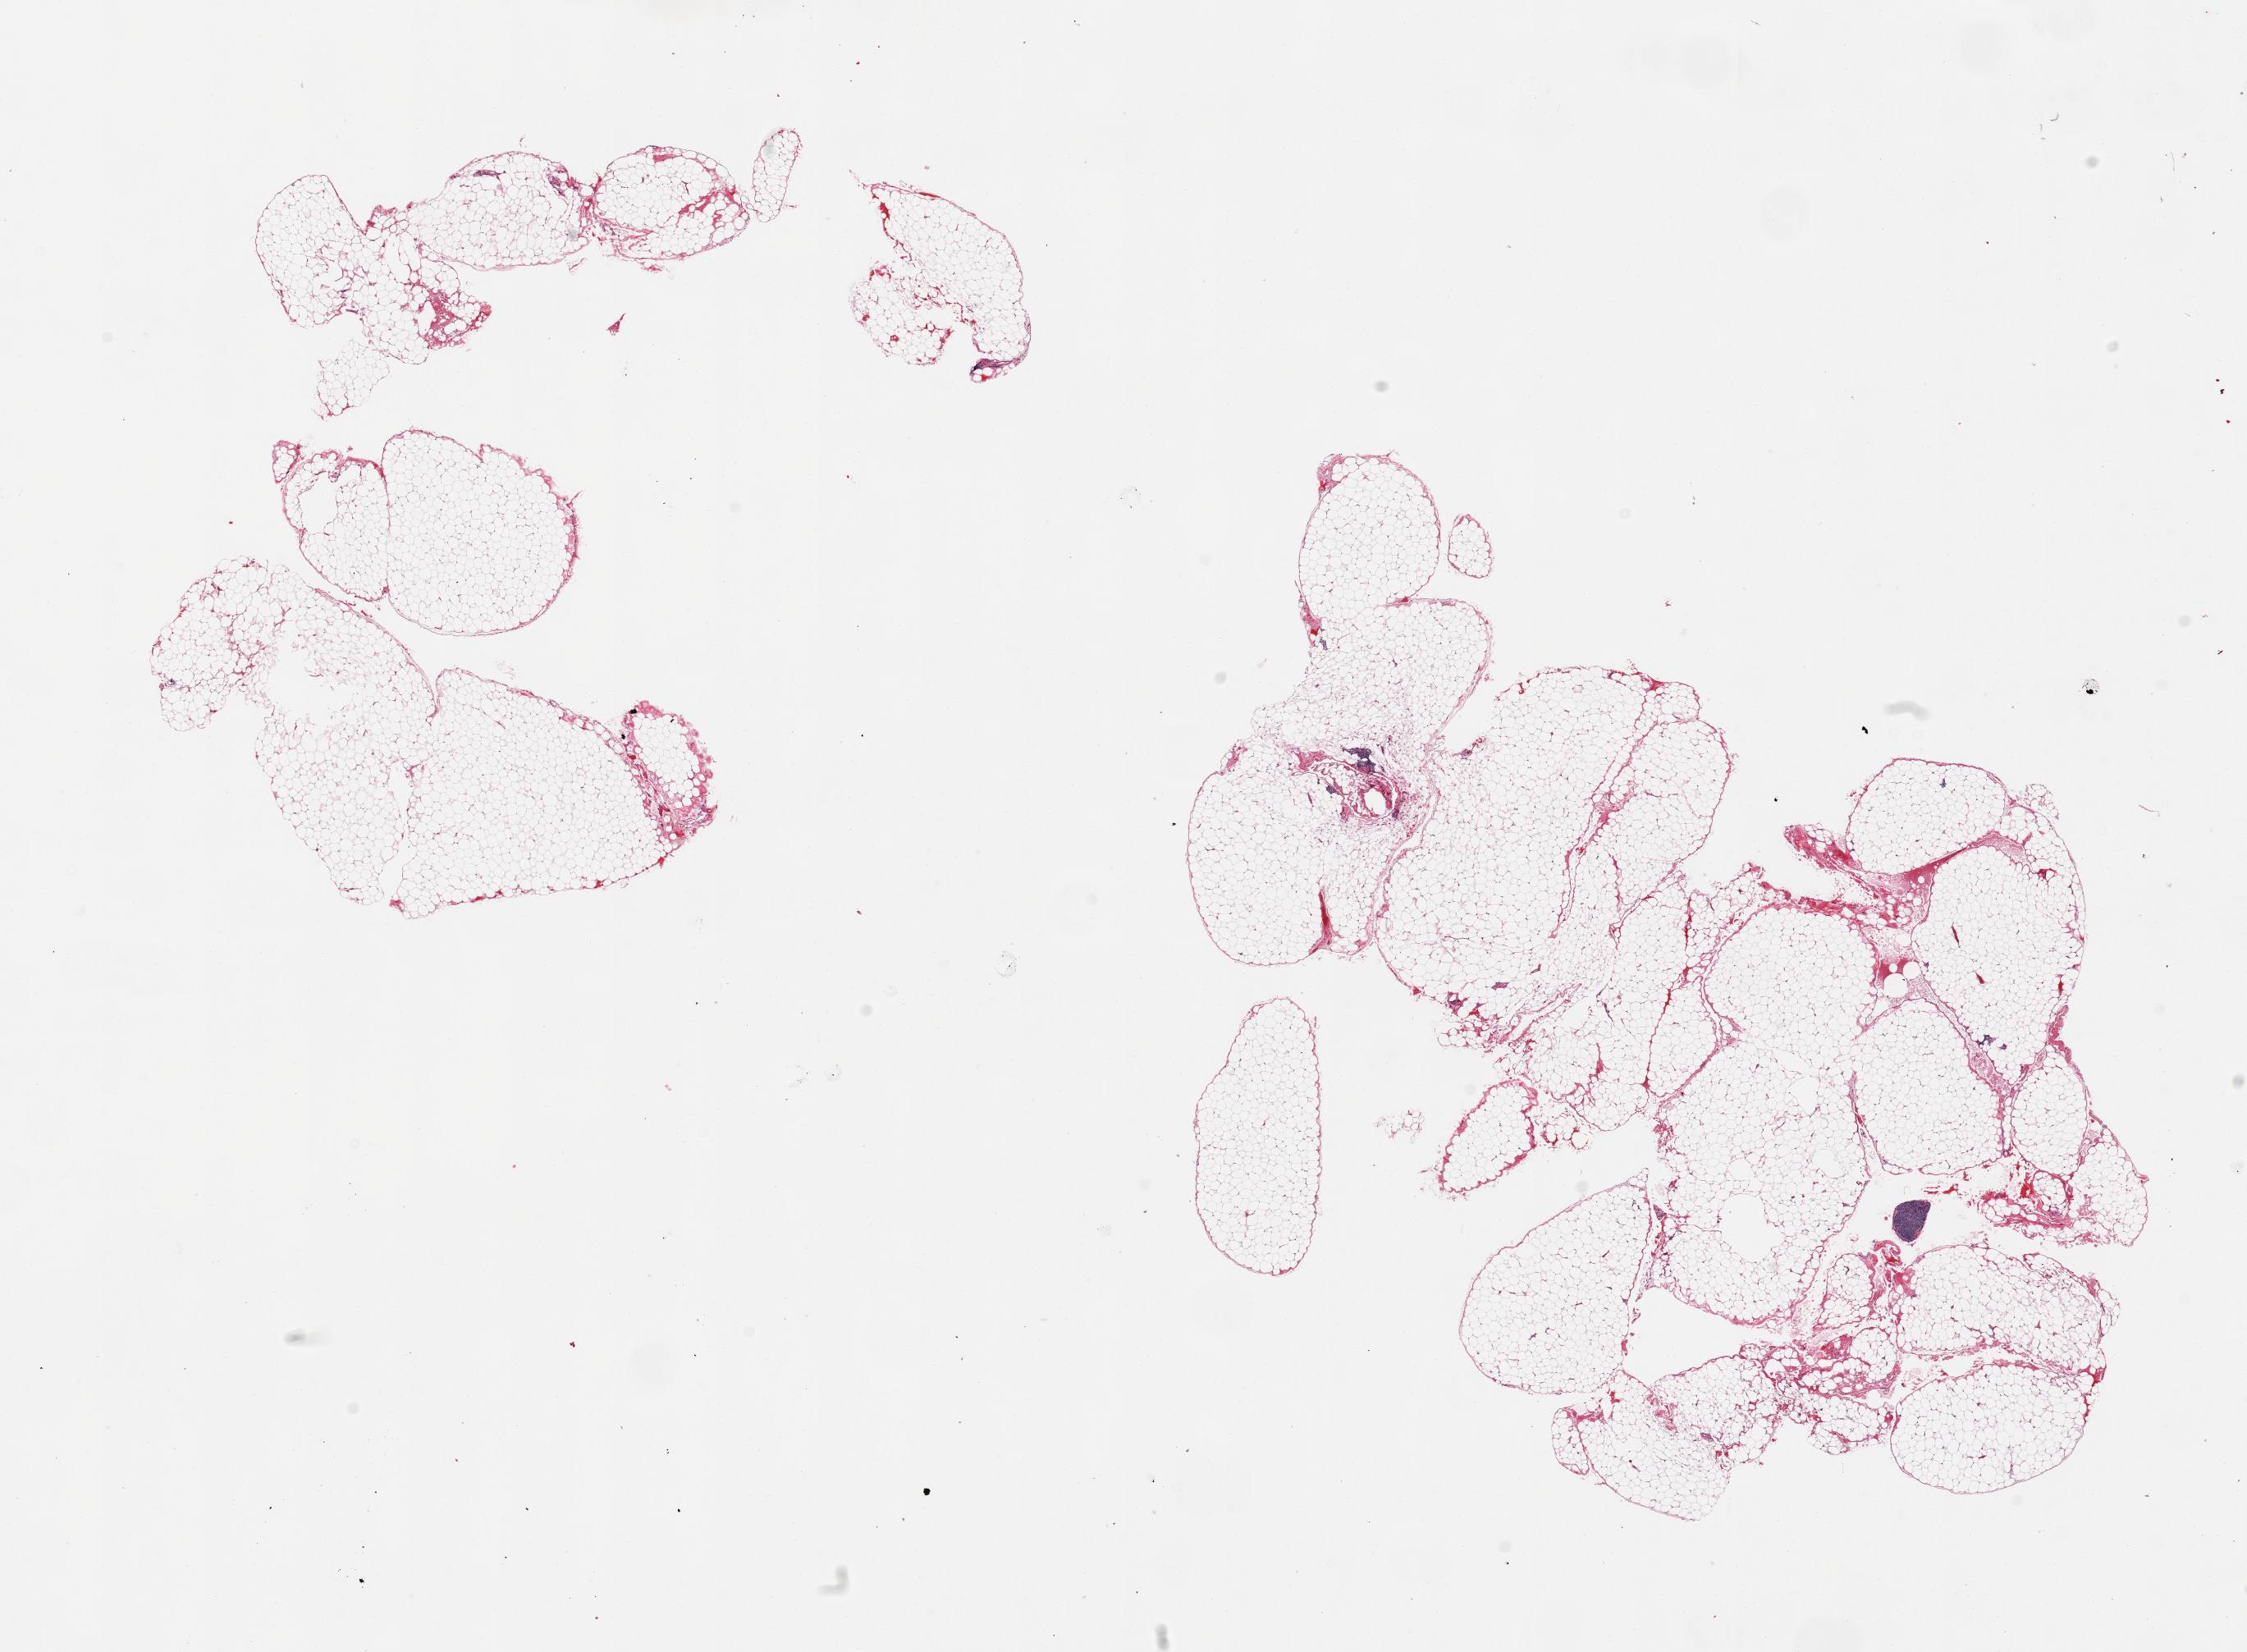
Whole-slide image, H&E stain, whole scanned area (about 21.7 x 15.9 mm) shown as a low-resolution overview. PAXgene-fixed, paraffin-embedded tissue. Sampled site (target tissue): omentum. Donor tissue sample. Donor: male.
- review note (as recorded): 2 pieces; small amount of fibrovascular tissue and rare lymphocytic aggregate